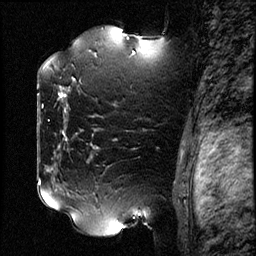
Breast MRI (dynamic contrast-enhanced), one sagittal slice; slice 58 of 78 in the series (ordered by position); dynamic contrast-enhanced study with each time point stored as its own series, time point 2 of 3 at this slice position (early post-contrast, ordered by acquisition time); 1.5 T; TE 4.2 ms, TR 17.6 ms; 2 mm slice thickness; 256 × 256 image matrix, field of view 200 × 200 mm. Patient: female, 42 years. Case-level facts recorded for this patient, not image findings: setting: breast cancer imaged before/during neoadjuvant chemotherapy; receptor status: HER2-positive.
Outlined on this slice (semi-automatic segmentation, software-assisted and operator-edited):
- analysis volume of interest (the breast-tissue region the enhancement analysis was run in; not a lesion): bounding box [x1, y1, x2, y2] px = [50, 48, 131, 129]
- tumour enhancement mask (voxels above the 100 % enhancement threshold inside the analysis volume of interest): [60, 78, 75, 98]